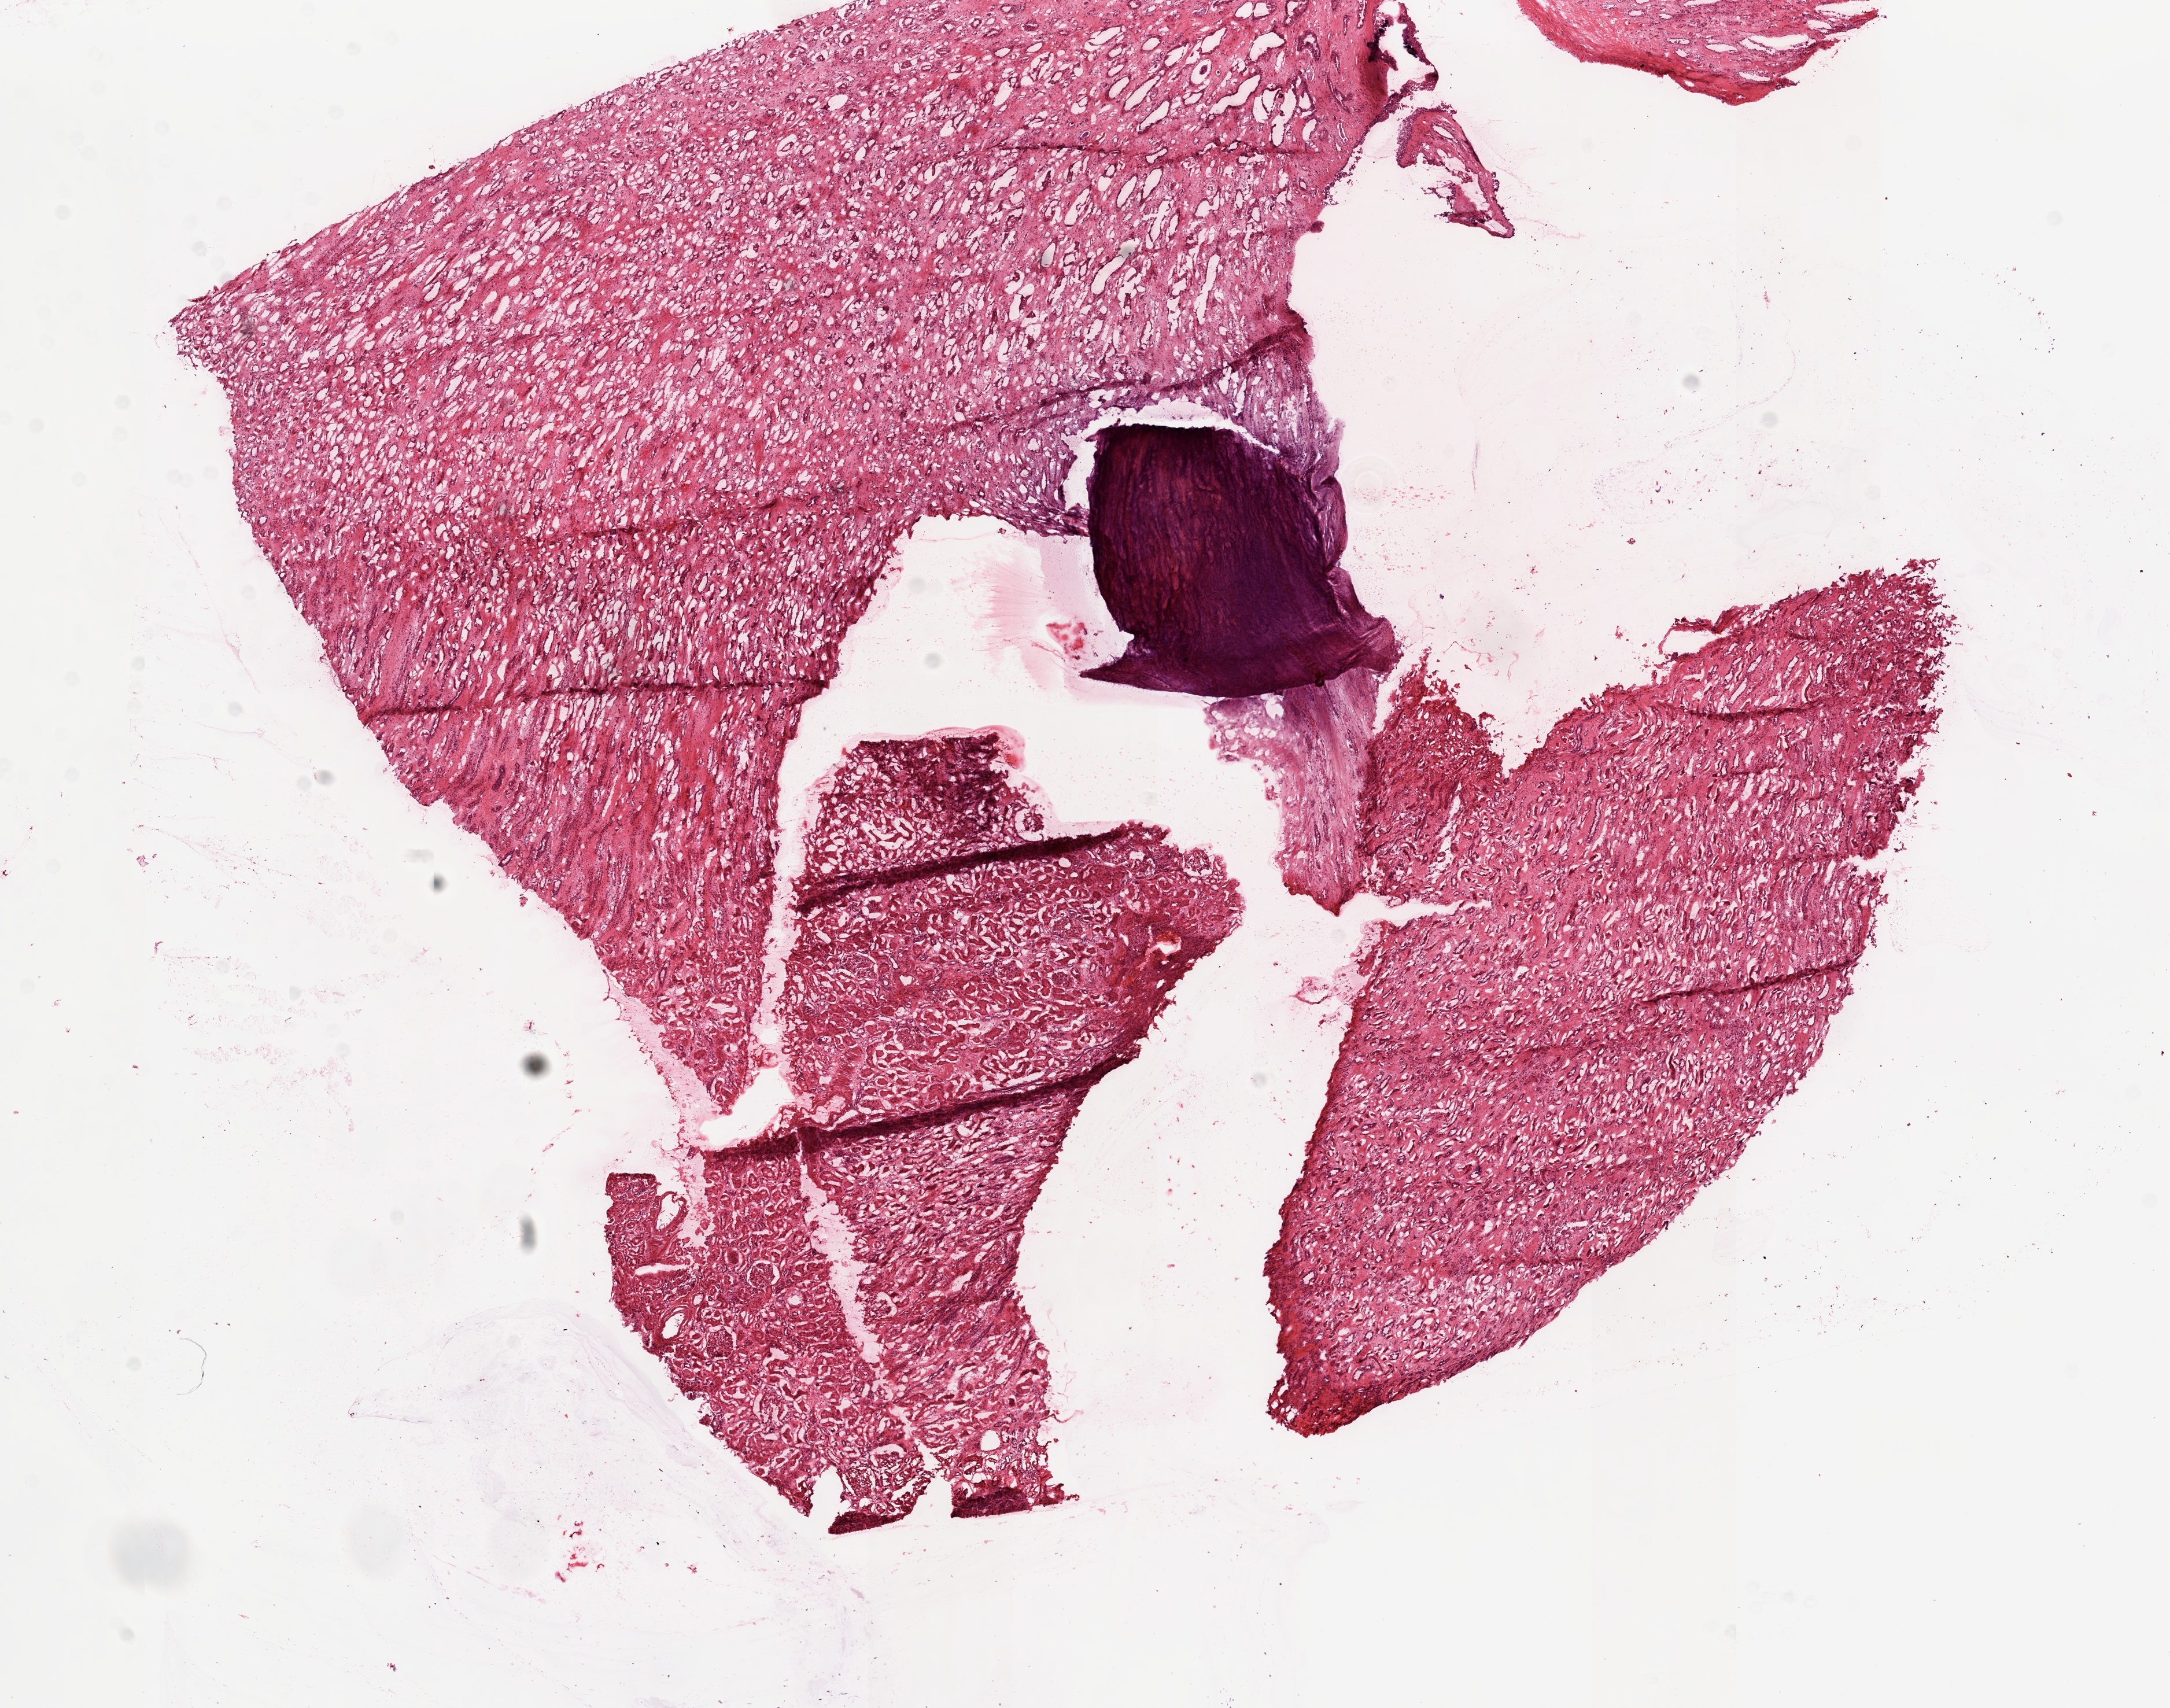
Digitized H&E tissue section (whole slide), whole scanned area (about 14.9 x 11.7 mm, slide scanned at 20x) shown as a low-resolution overview; frozen section from the top of the tissue portion; kidney, solid tissue normal (non-tumour tissue) sample. Male patient; age at initial diagnosis 72 years.
* this section: solid tissue normal (non-tumour) sample from the same patient
* patient diagnosis: Clear cell adenocarcinoma, NOS